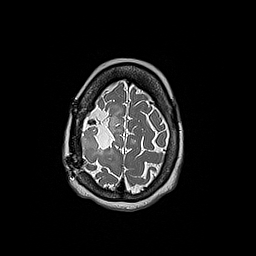
Brain MRI from a brain-tumour surgery series, one axial slice; position 47 of 192 along the scan axis; 1 mm slice thickness; 256 × 256 image matrix, field of view 250 × 250 mm. Case-level facts recorded for this patient, not image findings: histopathology: Oligodendroglioma; WHO grade: 3; IDH mutation: yes; tumour location: Right Frontal.
Structures marked on this image (manually delineated by an expert):
- tumour: bounding box (x1, y1, x2, y2) in pixels: (81, 113, 99, 152)